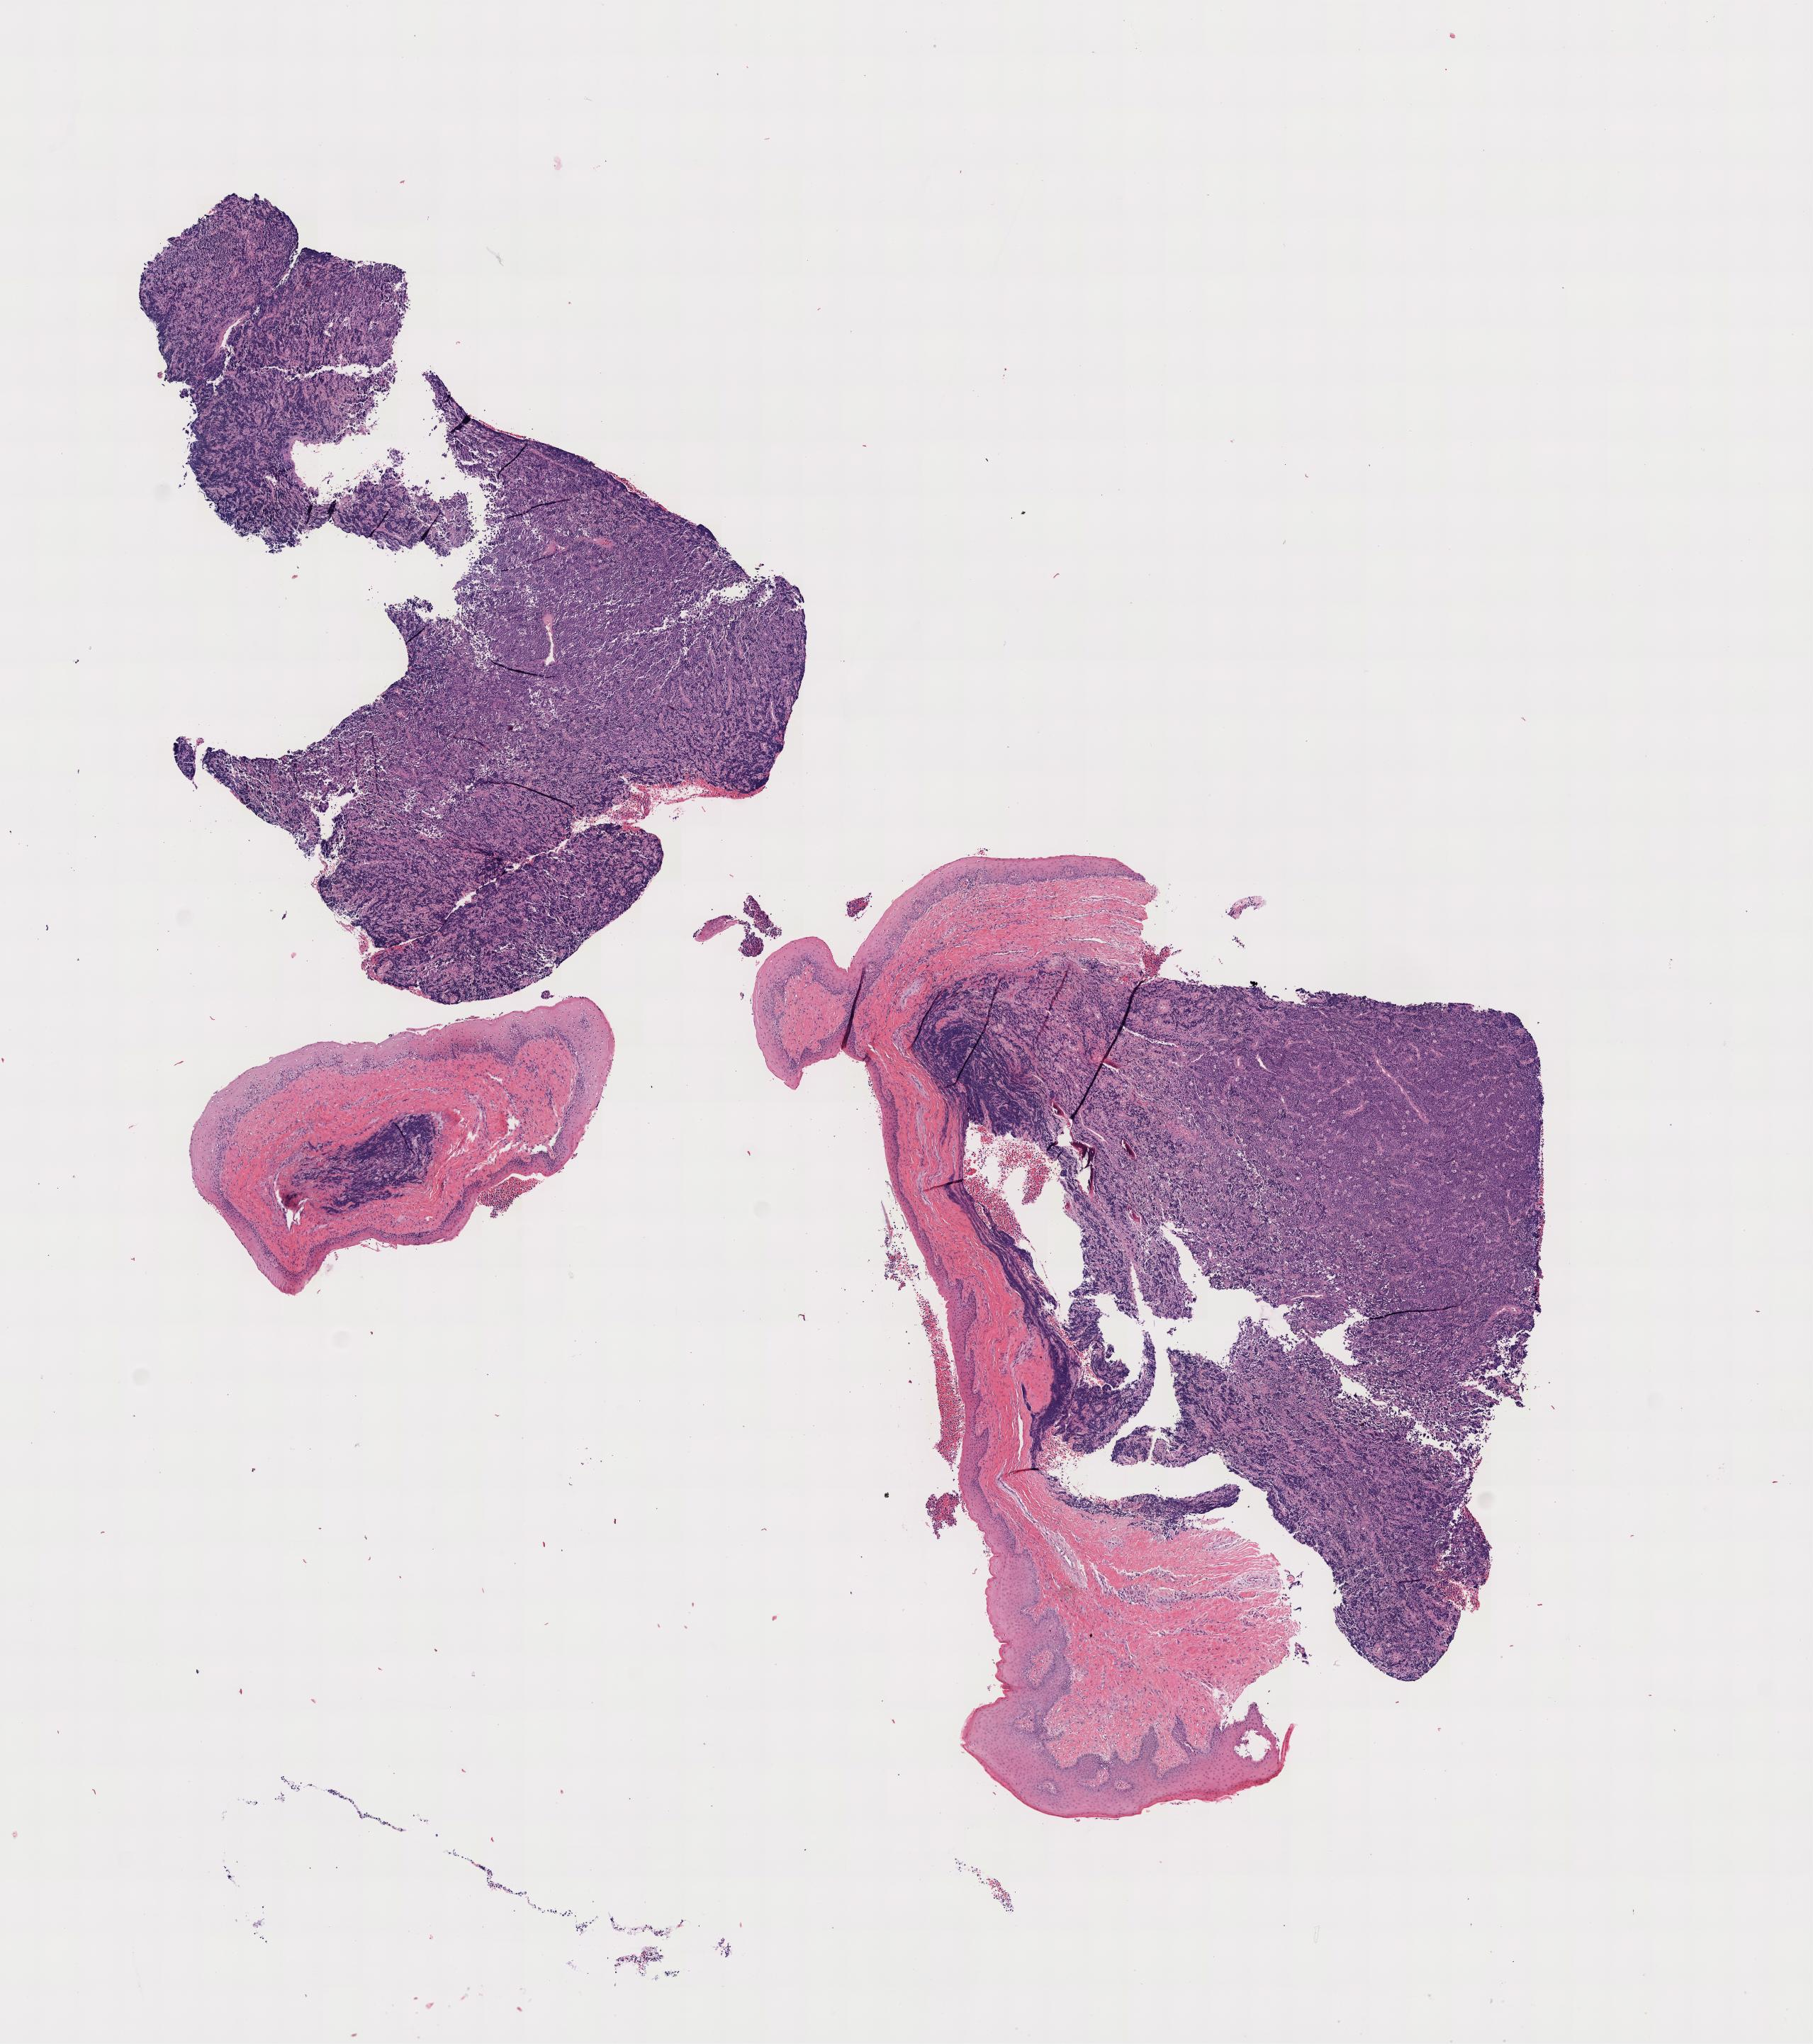
Digitized hematoxylin and eosin (H&E)-stained section — whole scanned area shown as a low-resolution overview; tumor tissue; site: mandible. Male, age 9 years at initial diagnosis.
Histologic diagnosis: Burkitt lymphoma, NOS.